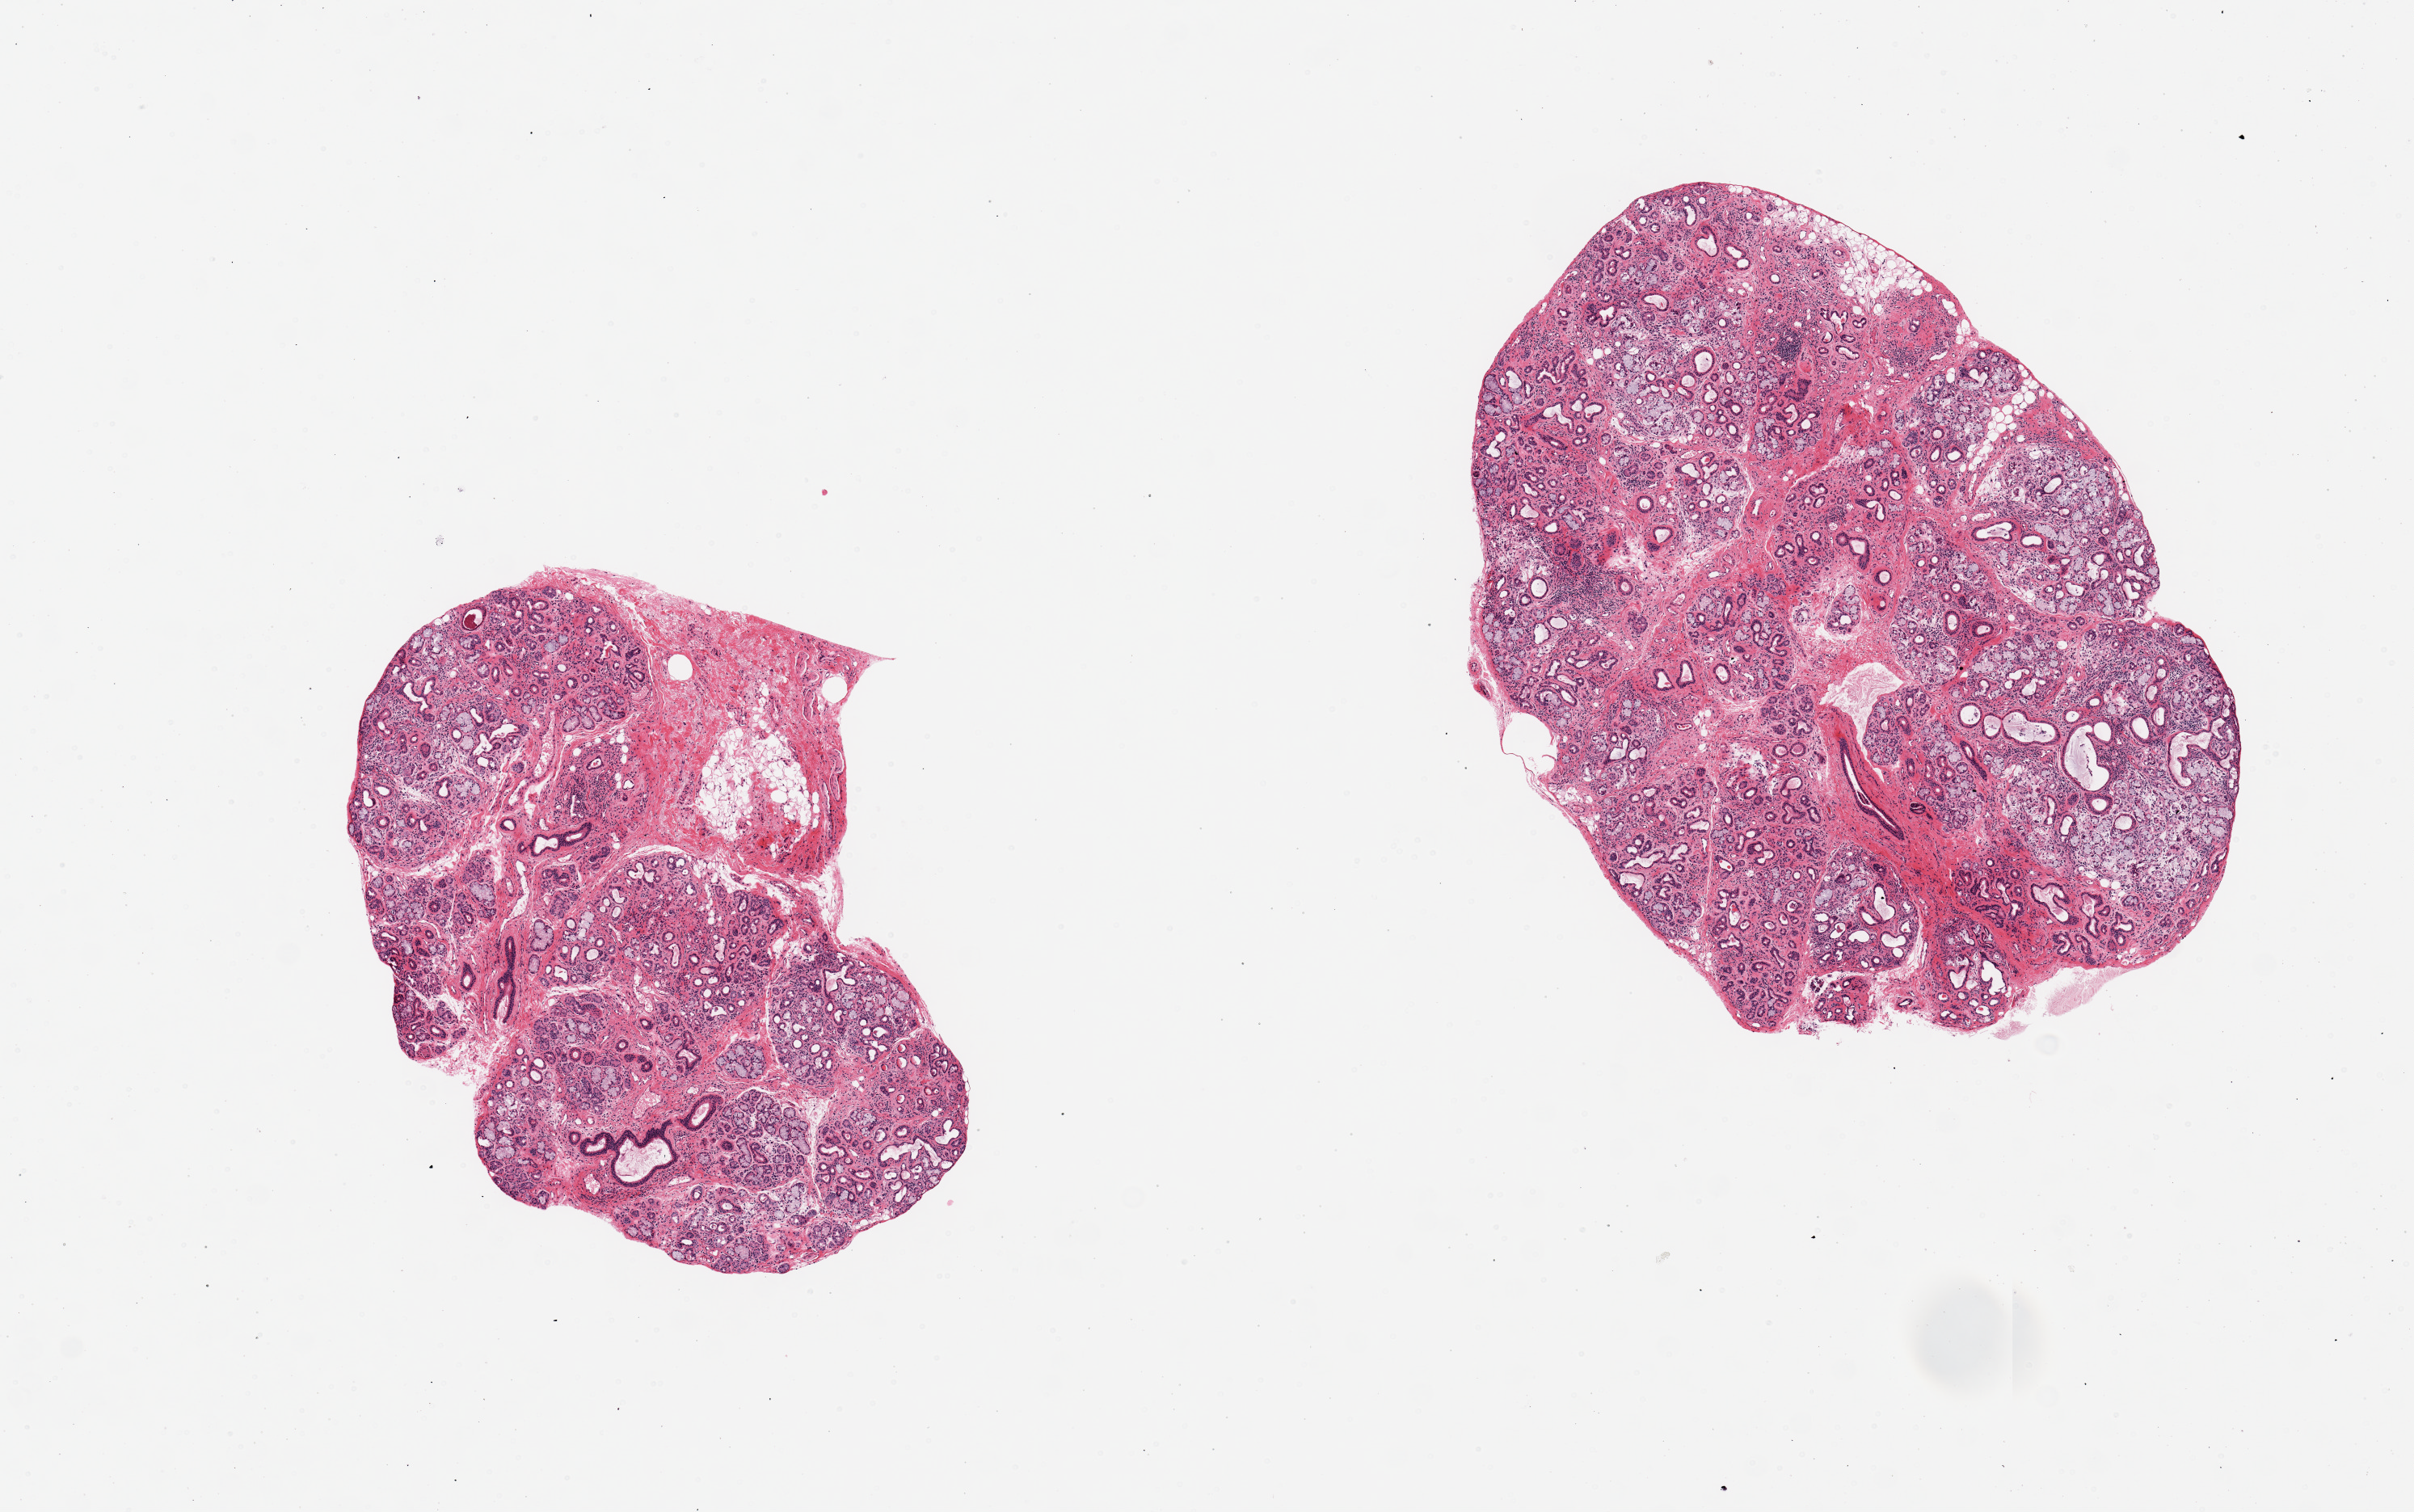
Whole-slide image, hematoxylin and eosin (H&E) stain — shown as a low-resolution overview of the whole scanned area (about 11.8 x 7.4 mm, from a 20x scan); PAXgene-fixed paraffin-embedded (PFPE) section; target tissue: minor salivary gland; donor tissue sample. Female donor.
Pathologist's review note for this sample: 2 pieces, generally good, one aliquot has ~25% adherent nubbing of adipose/muscular tissue.